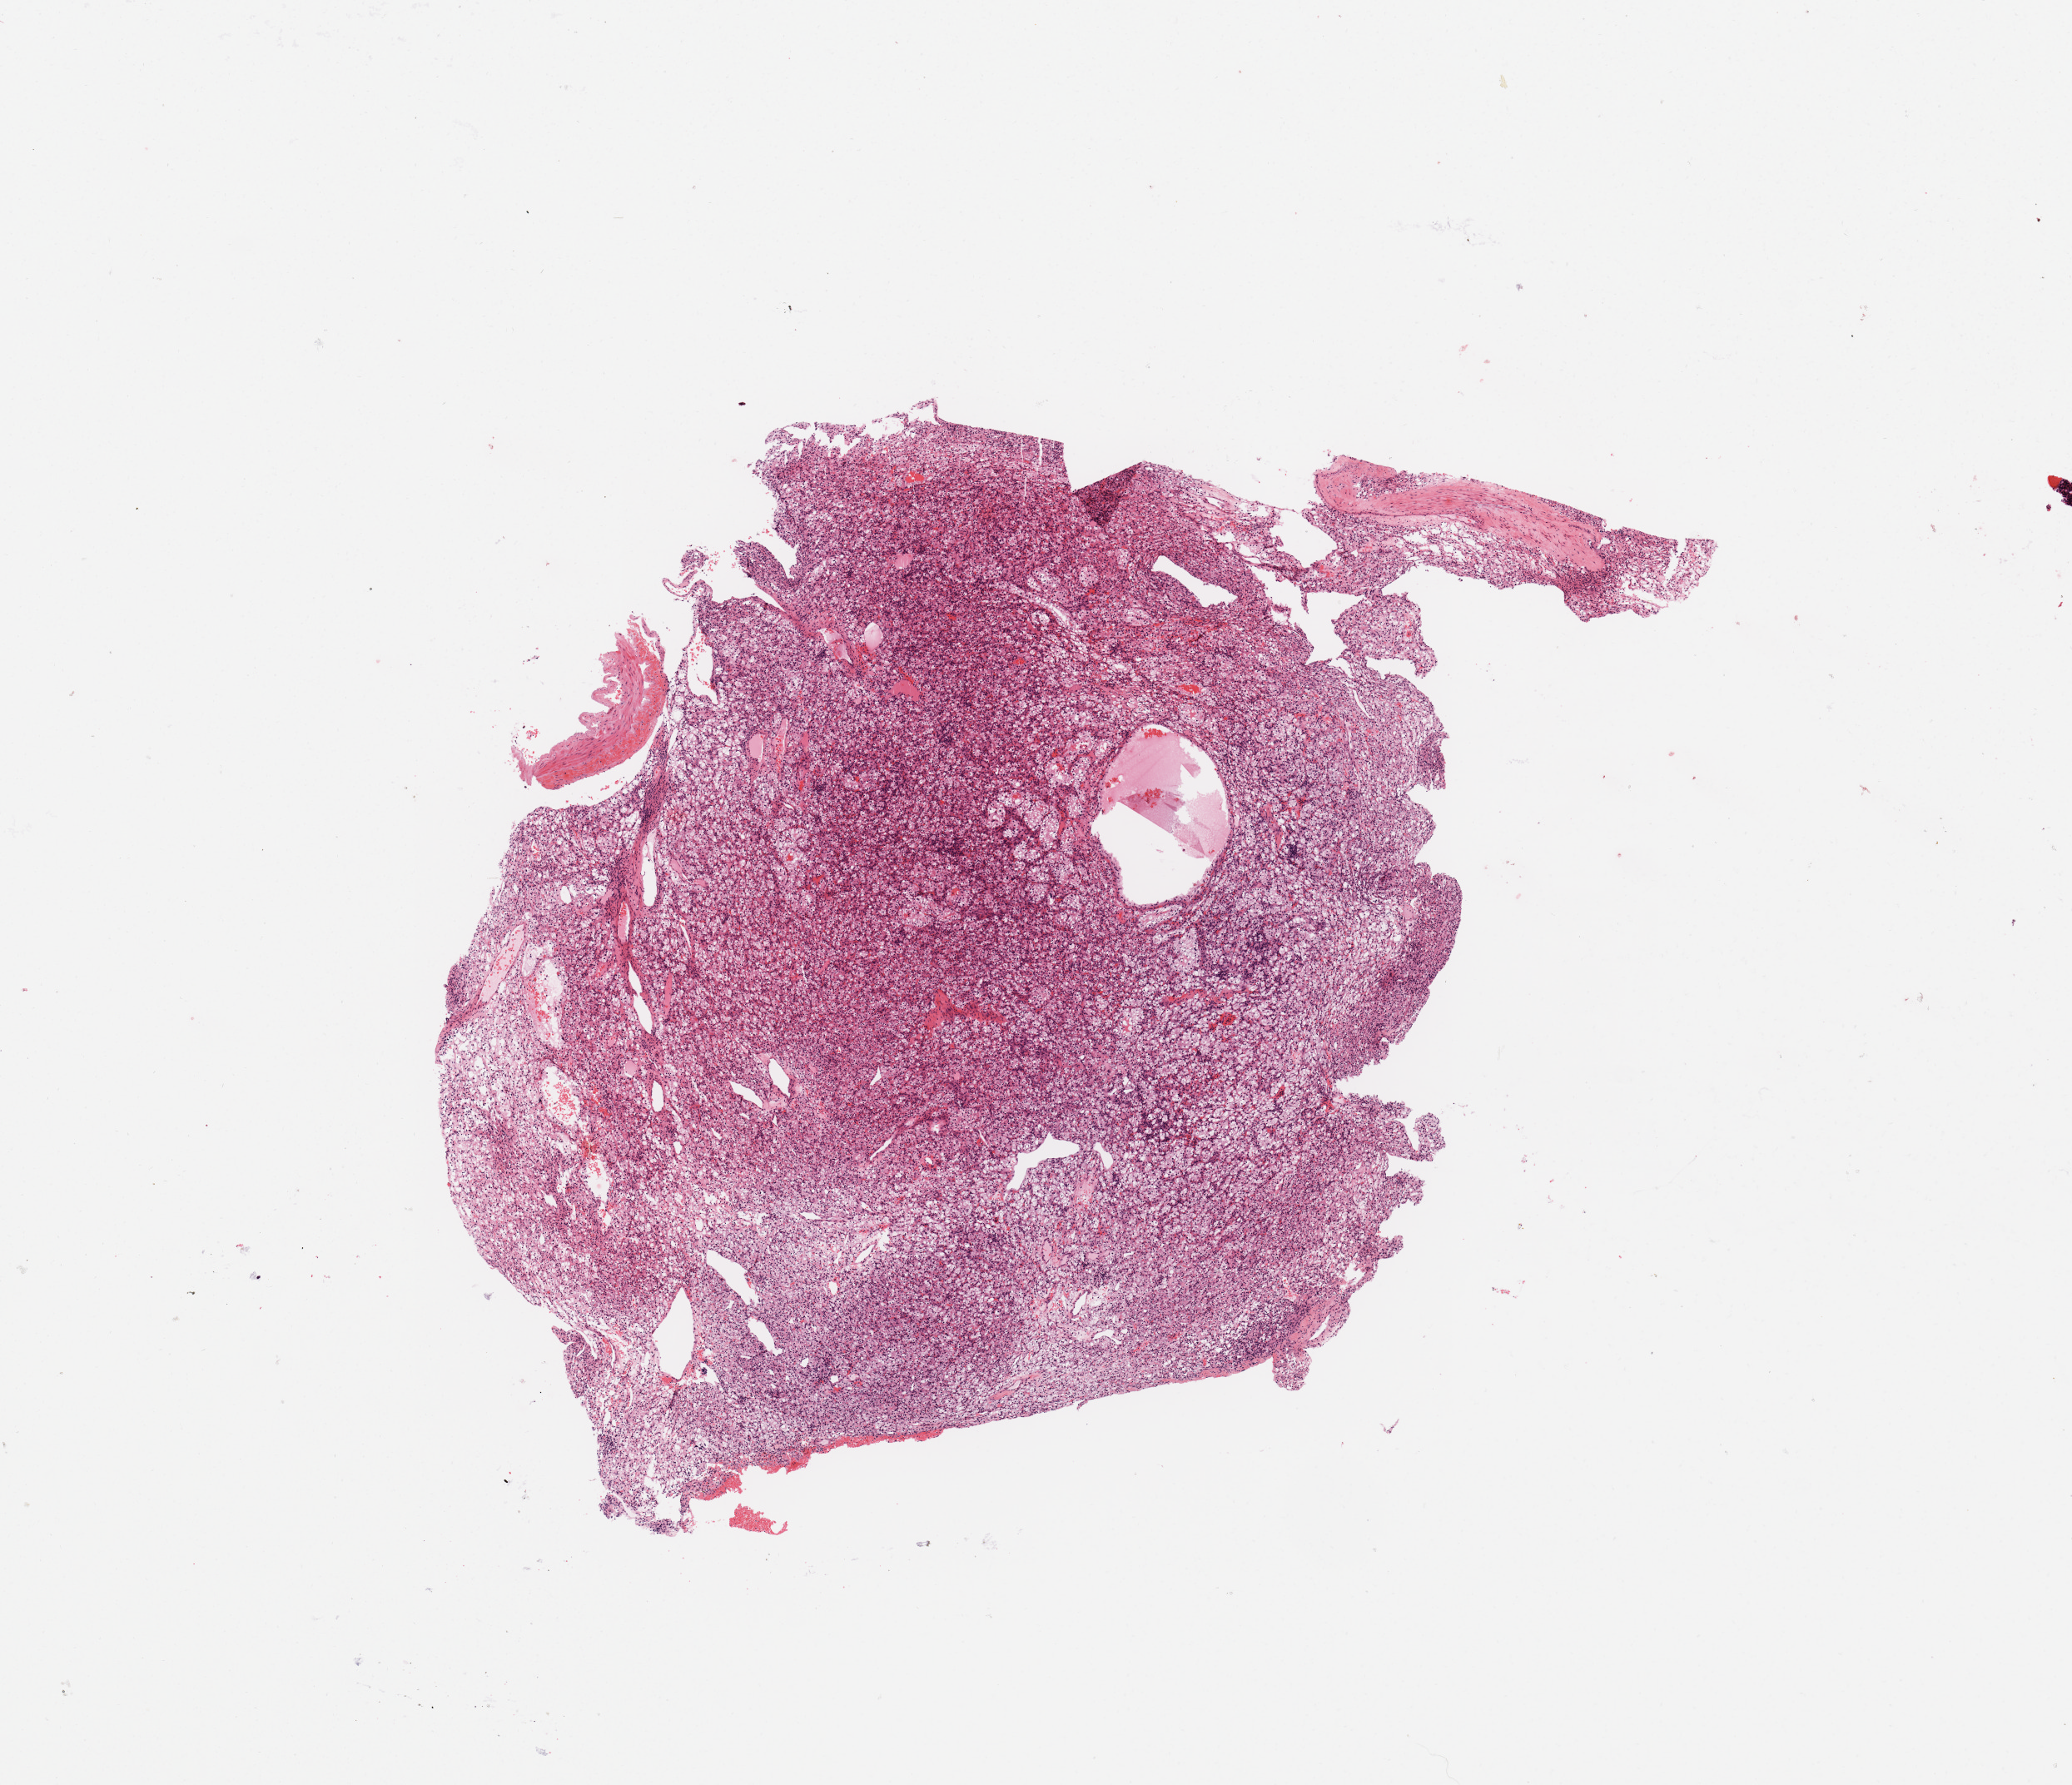
Hematoxylin and eosin (H&E) stained whole-slide image, whole scanned area (about 9.8 x 8.5 mm, slide scanned at 20x) shown as a low-resolution overview. Tumour tissue sample, sampled site: kidney. Female, 66 y/o. Histologic grade: G2 (moderately differentiated). Slide review estimates, as recorded: tumour nuclei 95%, necrosis 0%.
Histologic diagnosis: Renal cell carcinoma, NOS. AJCC pathologic stage: I. Primary tumour site (as recorded): lower pole.